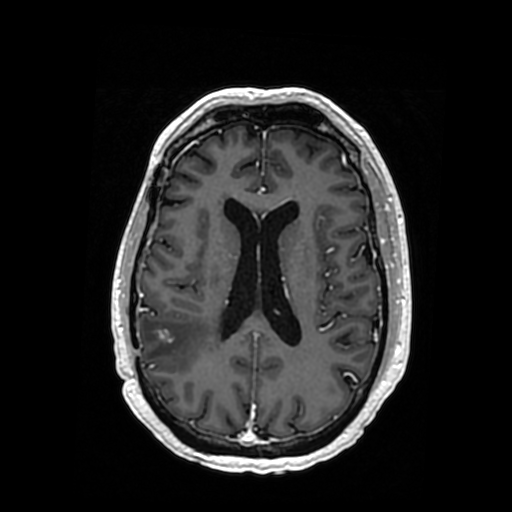
Brain MRI from a brain-tumour surgery series, one axial slice. Slice 152 of 364 in the series (ordered by position). T1-weighted post-contrast. 512 × 512 image matrix, field of view 260 × 260 mm. Case-level facts recorded for this patient, not image findings: histopathology: Oligodendroglioma; WHO grade: 3.
Annotated regions visible in this slice (manually delineated by an expert):
- tumour: bounding box <166,329,180,341> (left, top, right, bottom; pixels)